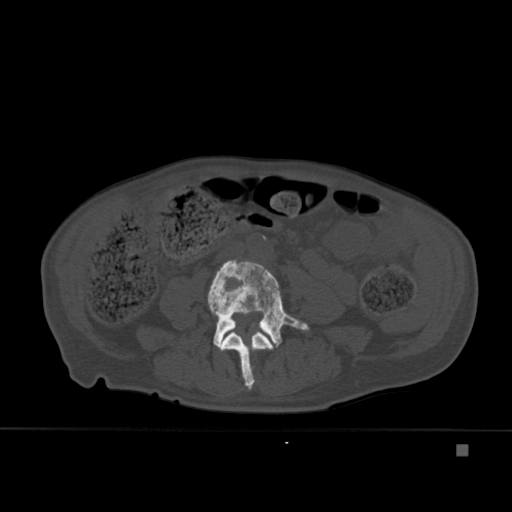
CT including the spine, one axial slice; position 130 of 451 along the scan axis; bone window (W 1800 / L 400 HU); 512 × 512 image matrix. Male patient, age 75 years. Case-level facts recorded for this patient, not image findings: primary cancer: prostate.
Structures marked on this image (semi-automatic segmentation, software-assisted and operator-edited):
- L3 vertebra: bounding box [x1, y1, x2, y2] px = [219, 331, 274, 390]
- L4 vertebra: [208, 259, 309, 349]